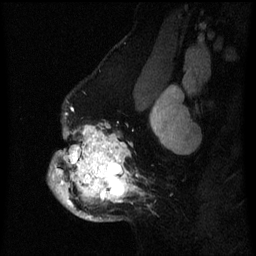
Breast MRI (dynamic contrast-enhanced), one sagittal slice. Slice 46 of 60 in the series (ordered by position). Dynamic contrast-enhanced series, image 2 of 3 at this slice position (ordered by acquisition). 1.5 T. TE 4.2 ms, TR 8 ms. 2 mm slice thickness. 256 × 256 image matrix. Patient: female, 50 years.
Annotated regions visible in this slice (semi-automatic segmentation, software-assisted and operator-edited):
- analysis volume of interest (the breast-tissue region the enhancement analysis was run in; not a lesion): bounding box [x1, y1, x2, y2] px = [48, 122, 140, 222]
- tumour enhancement mask (voxels above the 70 % enhancement threshold inside the analysis volume of interest): [49, 125, 136, 219]